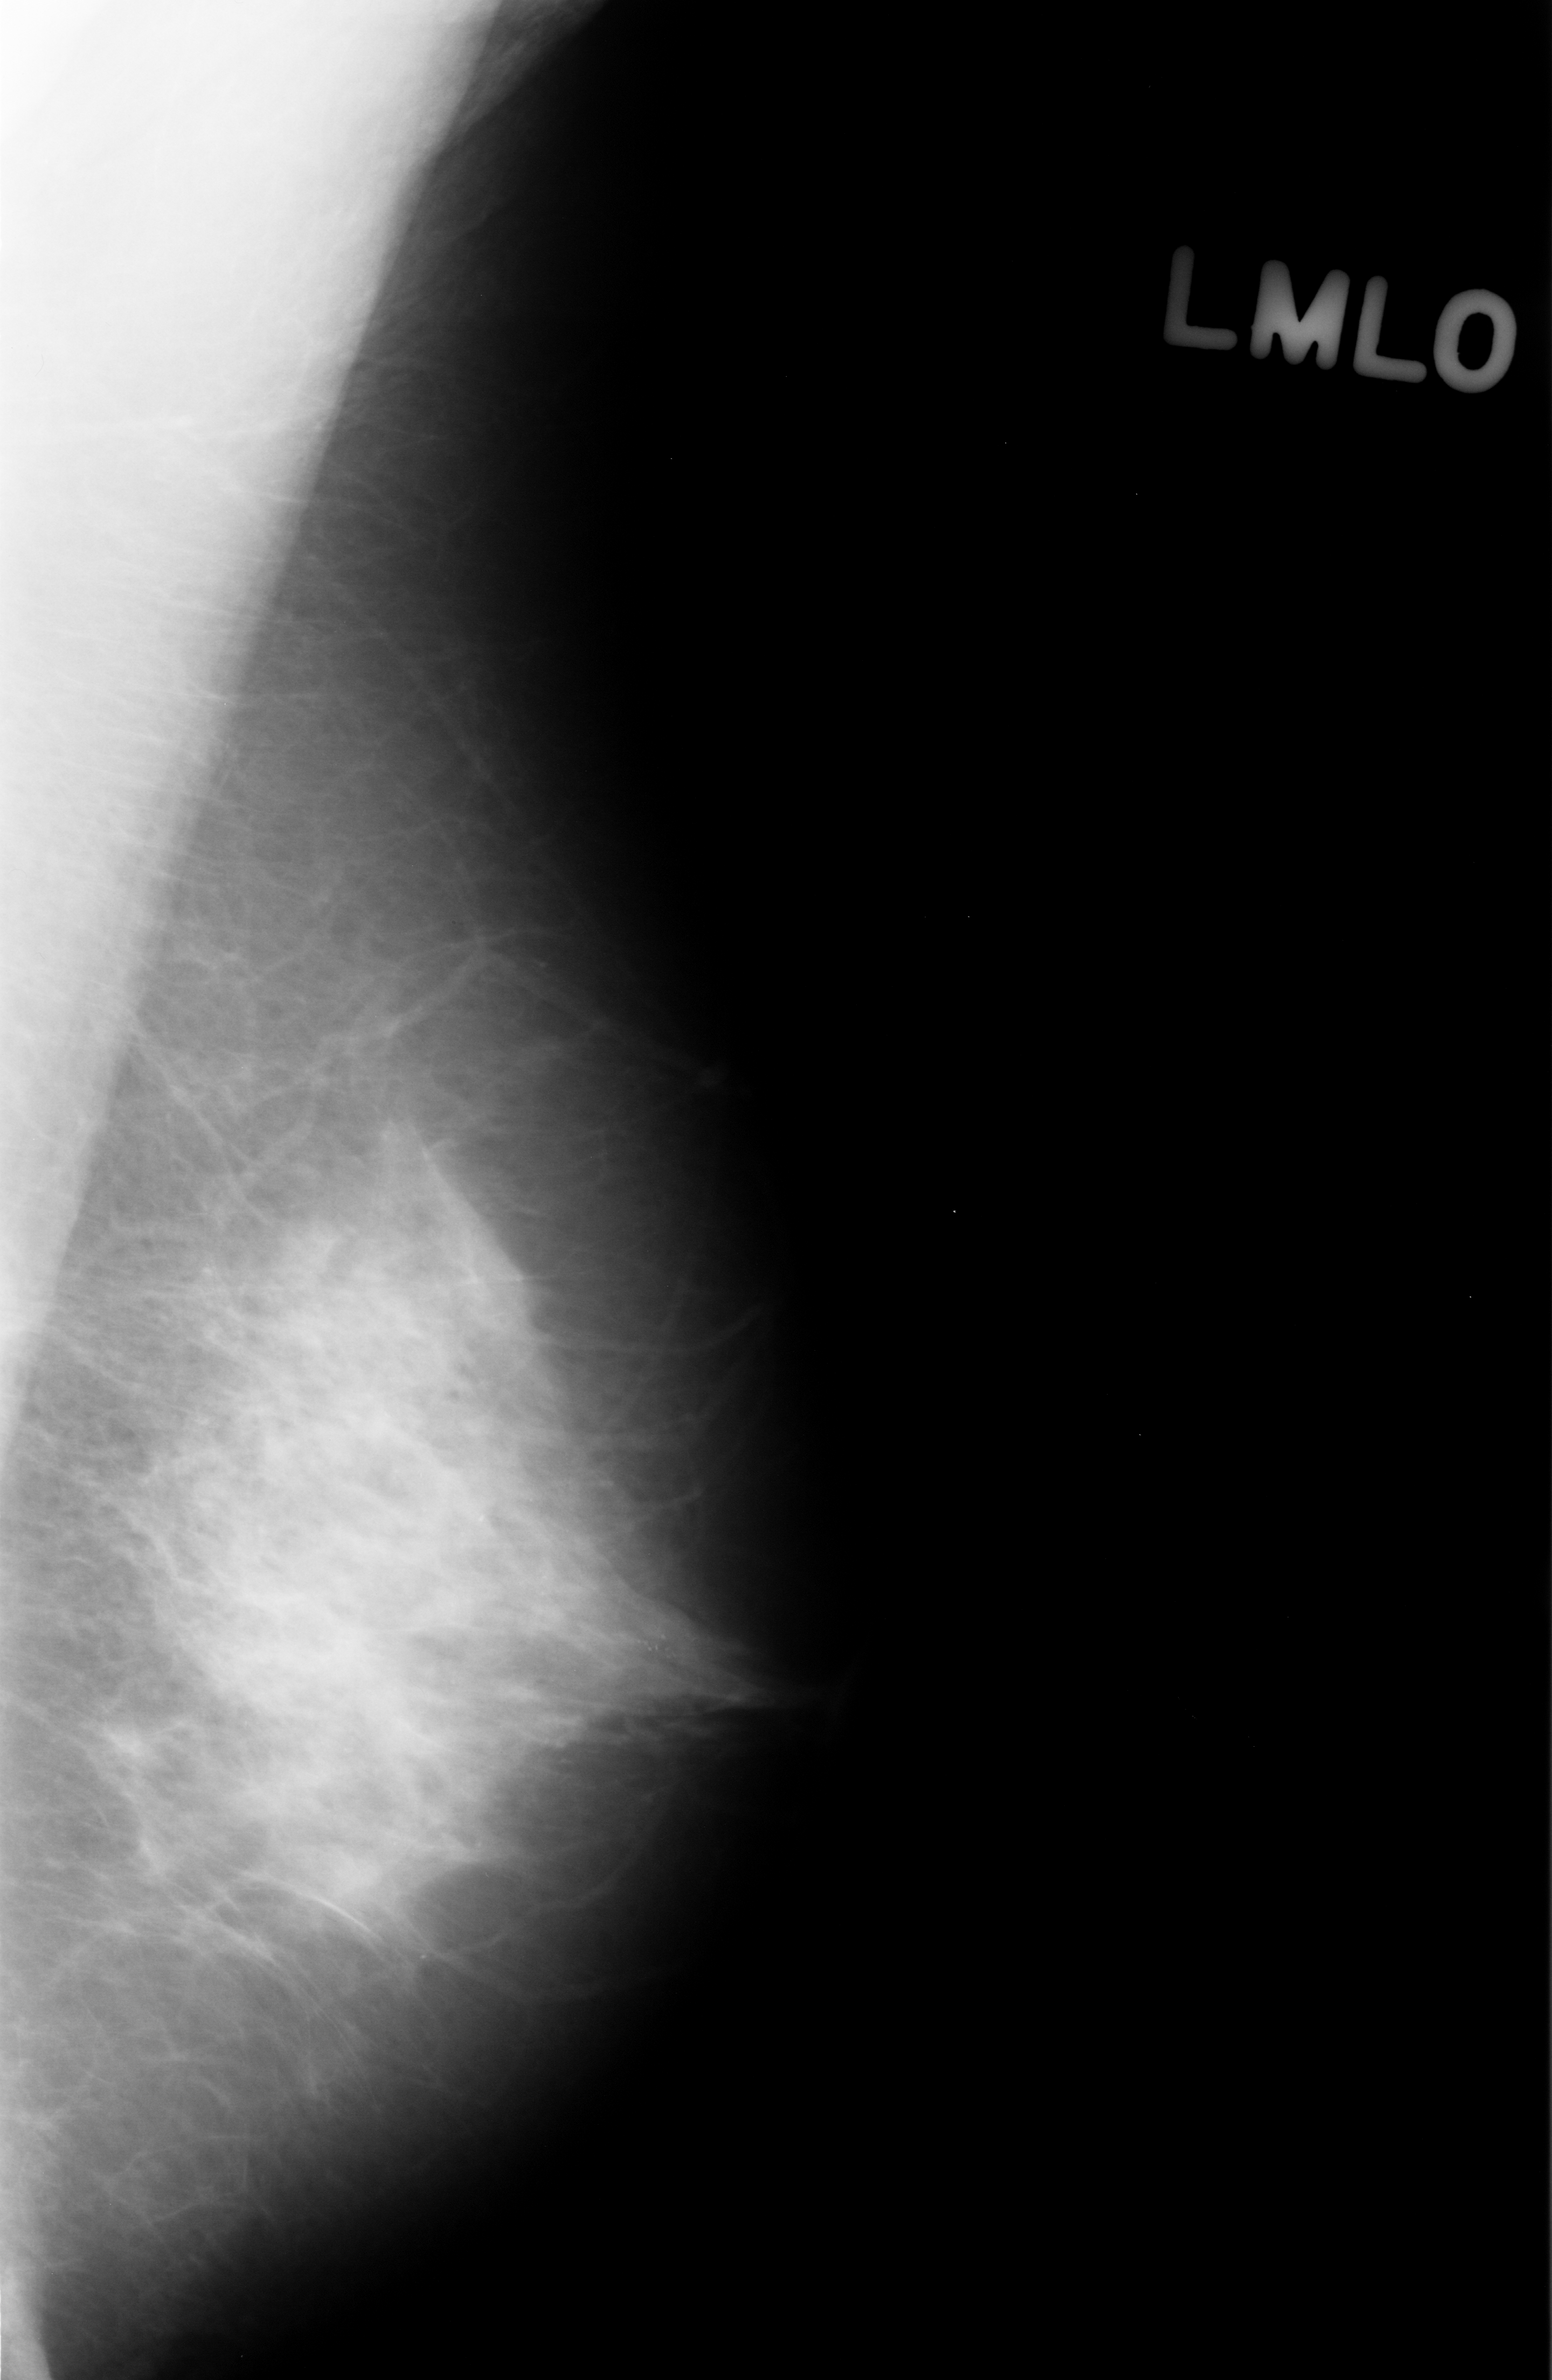
Digitized screen-film mammogram. Left breast. Mediolateral oblique (MLO) view. Breast composition: heterogeneously dense (BI-RADS density category 3 of 4). 1552 × 2380 image matrix.
Expert-marked regions of interest on this film, with their recorded descriptors:
- calcifications, morphology punctate, distribution clustered; BI-RADS assessment category 4; pathology (as recorded): benign: box from (x=521, y=1556) to (x=712, y=1769) px